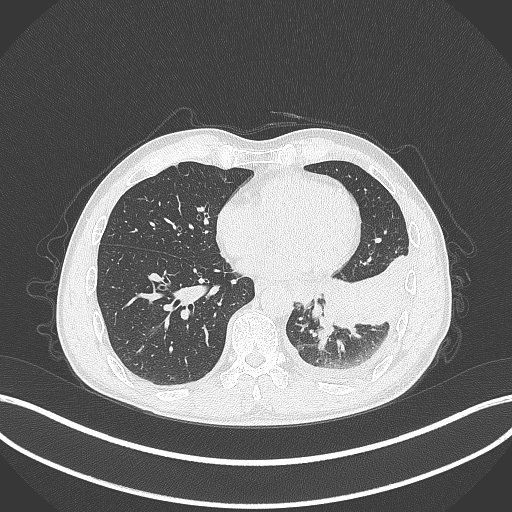
Chest CT, one axial slice. Slice 104 of 295 in the series (ordered by position). Reconstruction kernel B70f. Lung window (W 1500 / L -600 HU). 512 × 512 image matrix, field of view 400 × 400 mm. Male patient, age 47 years. Case-level facts recorded for this patient, not image findings: clinical TNM (as recorded): T3 N1 M1c; histopathological grade: G3.
Outlined on this slice (bounding box drawn by a radiologist):
- lung tumour (recorded histology: small cell carcinoma): bounding box (x1, y1, x2, y2) in pixels: (315, 312, 331, 328)